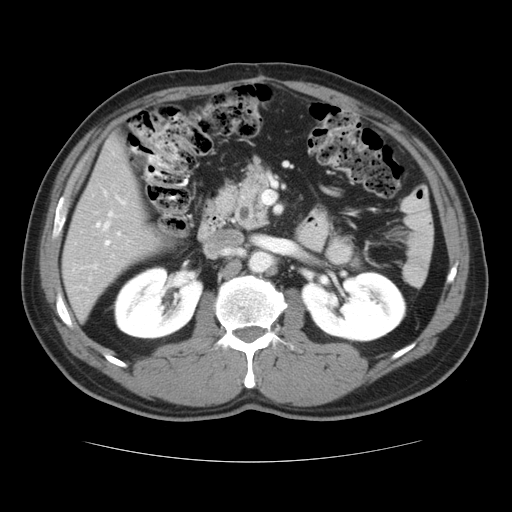
Contrast-enhanced abdominal CT, one axial slice; slice 16 of 37 in the series (ordered by position); reconstruction kernel STANDARD; 120 kVp; intravenous contrast given; soft-tissue window (W 400 / L 40 HU); 512 × 512 image matrix, field of view 374 × 374 mm. Male patient, age 66 years. Case-level facts recorded for this patient, not image findings: diagnosis: colorectal cancer liver metastases, imaged before liver resection; multiple liver metastases: yes; largest metastasis: 1.6 cm; disease in both lobes: yes.
Structures marked on this image (manually delineated by an expert):
- hepatic veins: bounding box <102,191,115,233> (left, top, right, bottom; pixels)
- liver: <62,135,164,320>
- planned liver remnant (the part of the liver to remain after resection): <62,193,165,320>
- portal vein (with intrahepatic branches): <96,199,125,245>